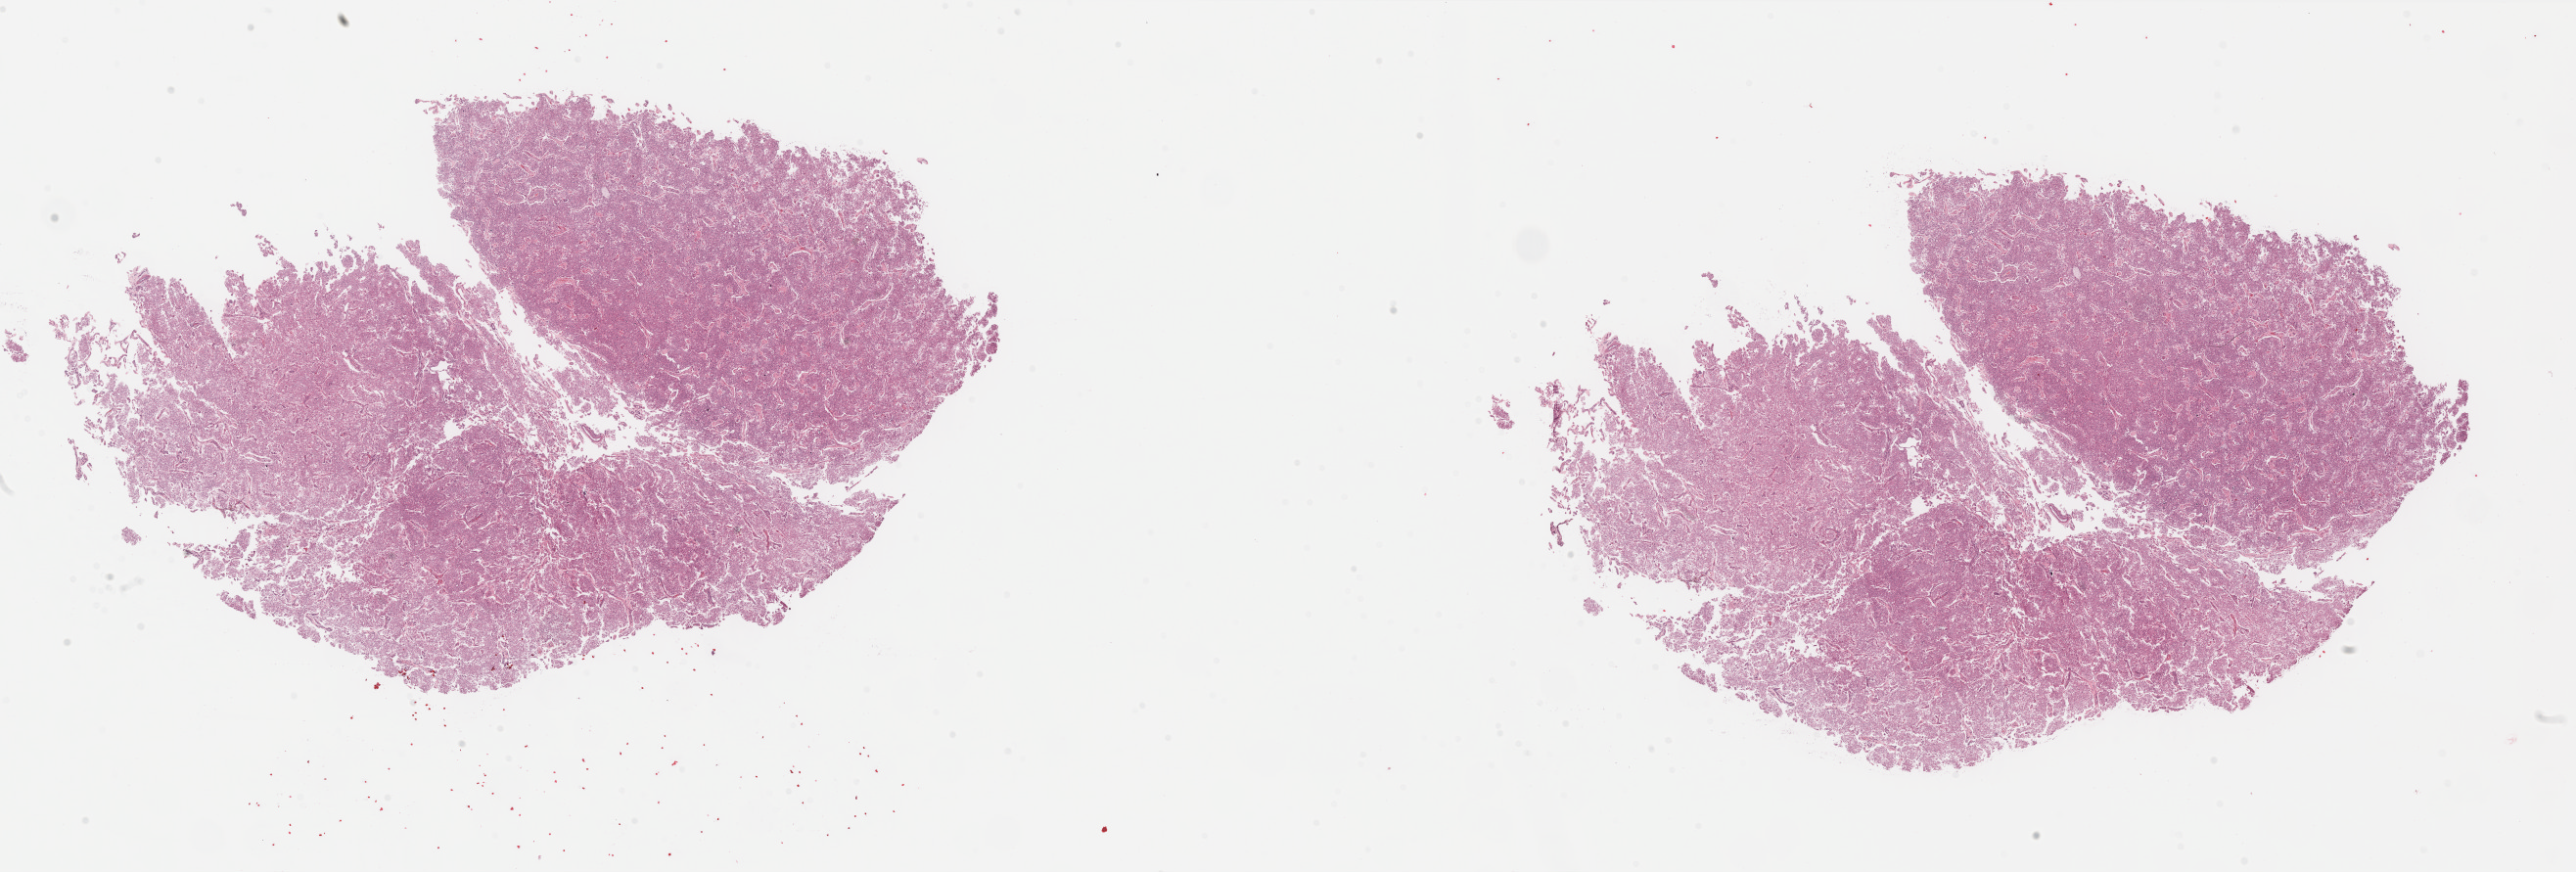
Digitized Hematoxylin and eosin (H&E) stained tissue section (whole slide) — low-resolution overview of the scanned area, about 41.7 x 14.1 mm (from a 40x scan); FFPE section; kidney, primary tumour sample. Male patient; age at initial diagnosis 45 years.
* histologic diagnosis: Renal cell carcinoma, chromophobe type
* AJCC pathologic stage: I (7th edition)
* laterality: left